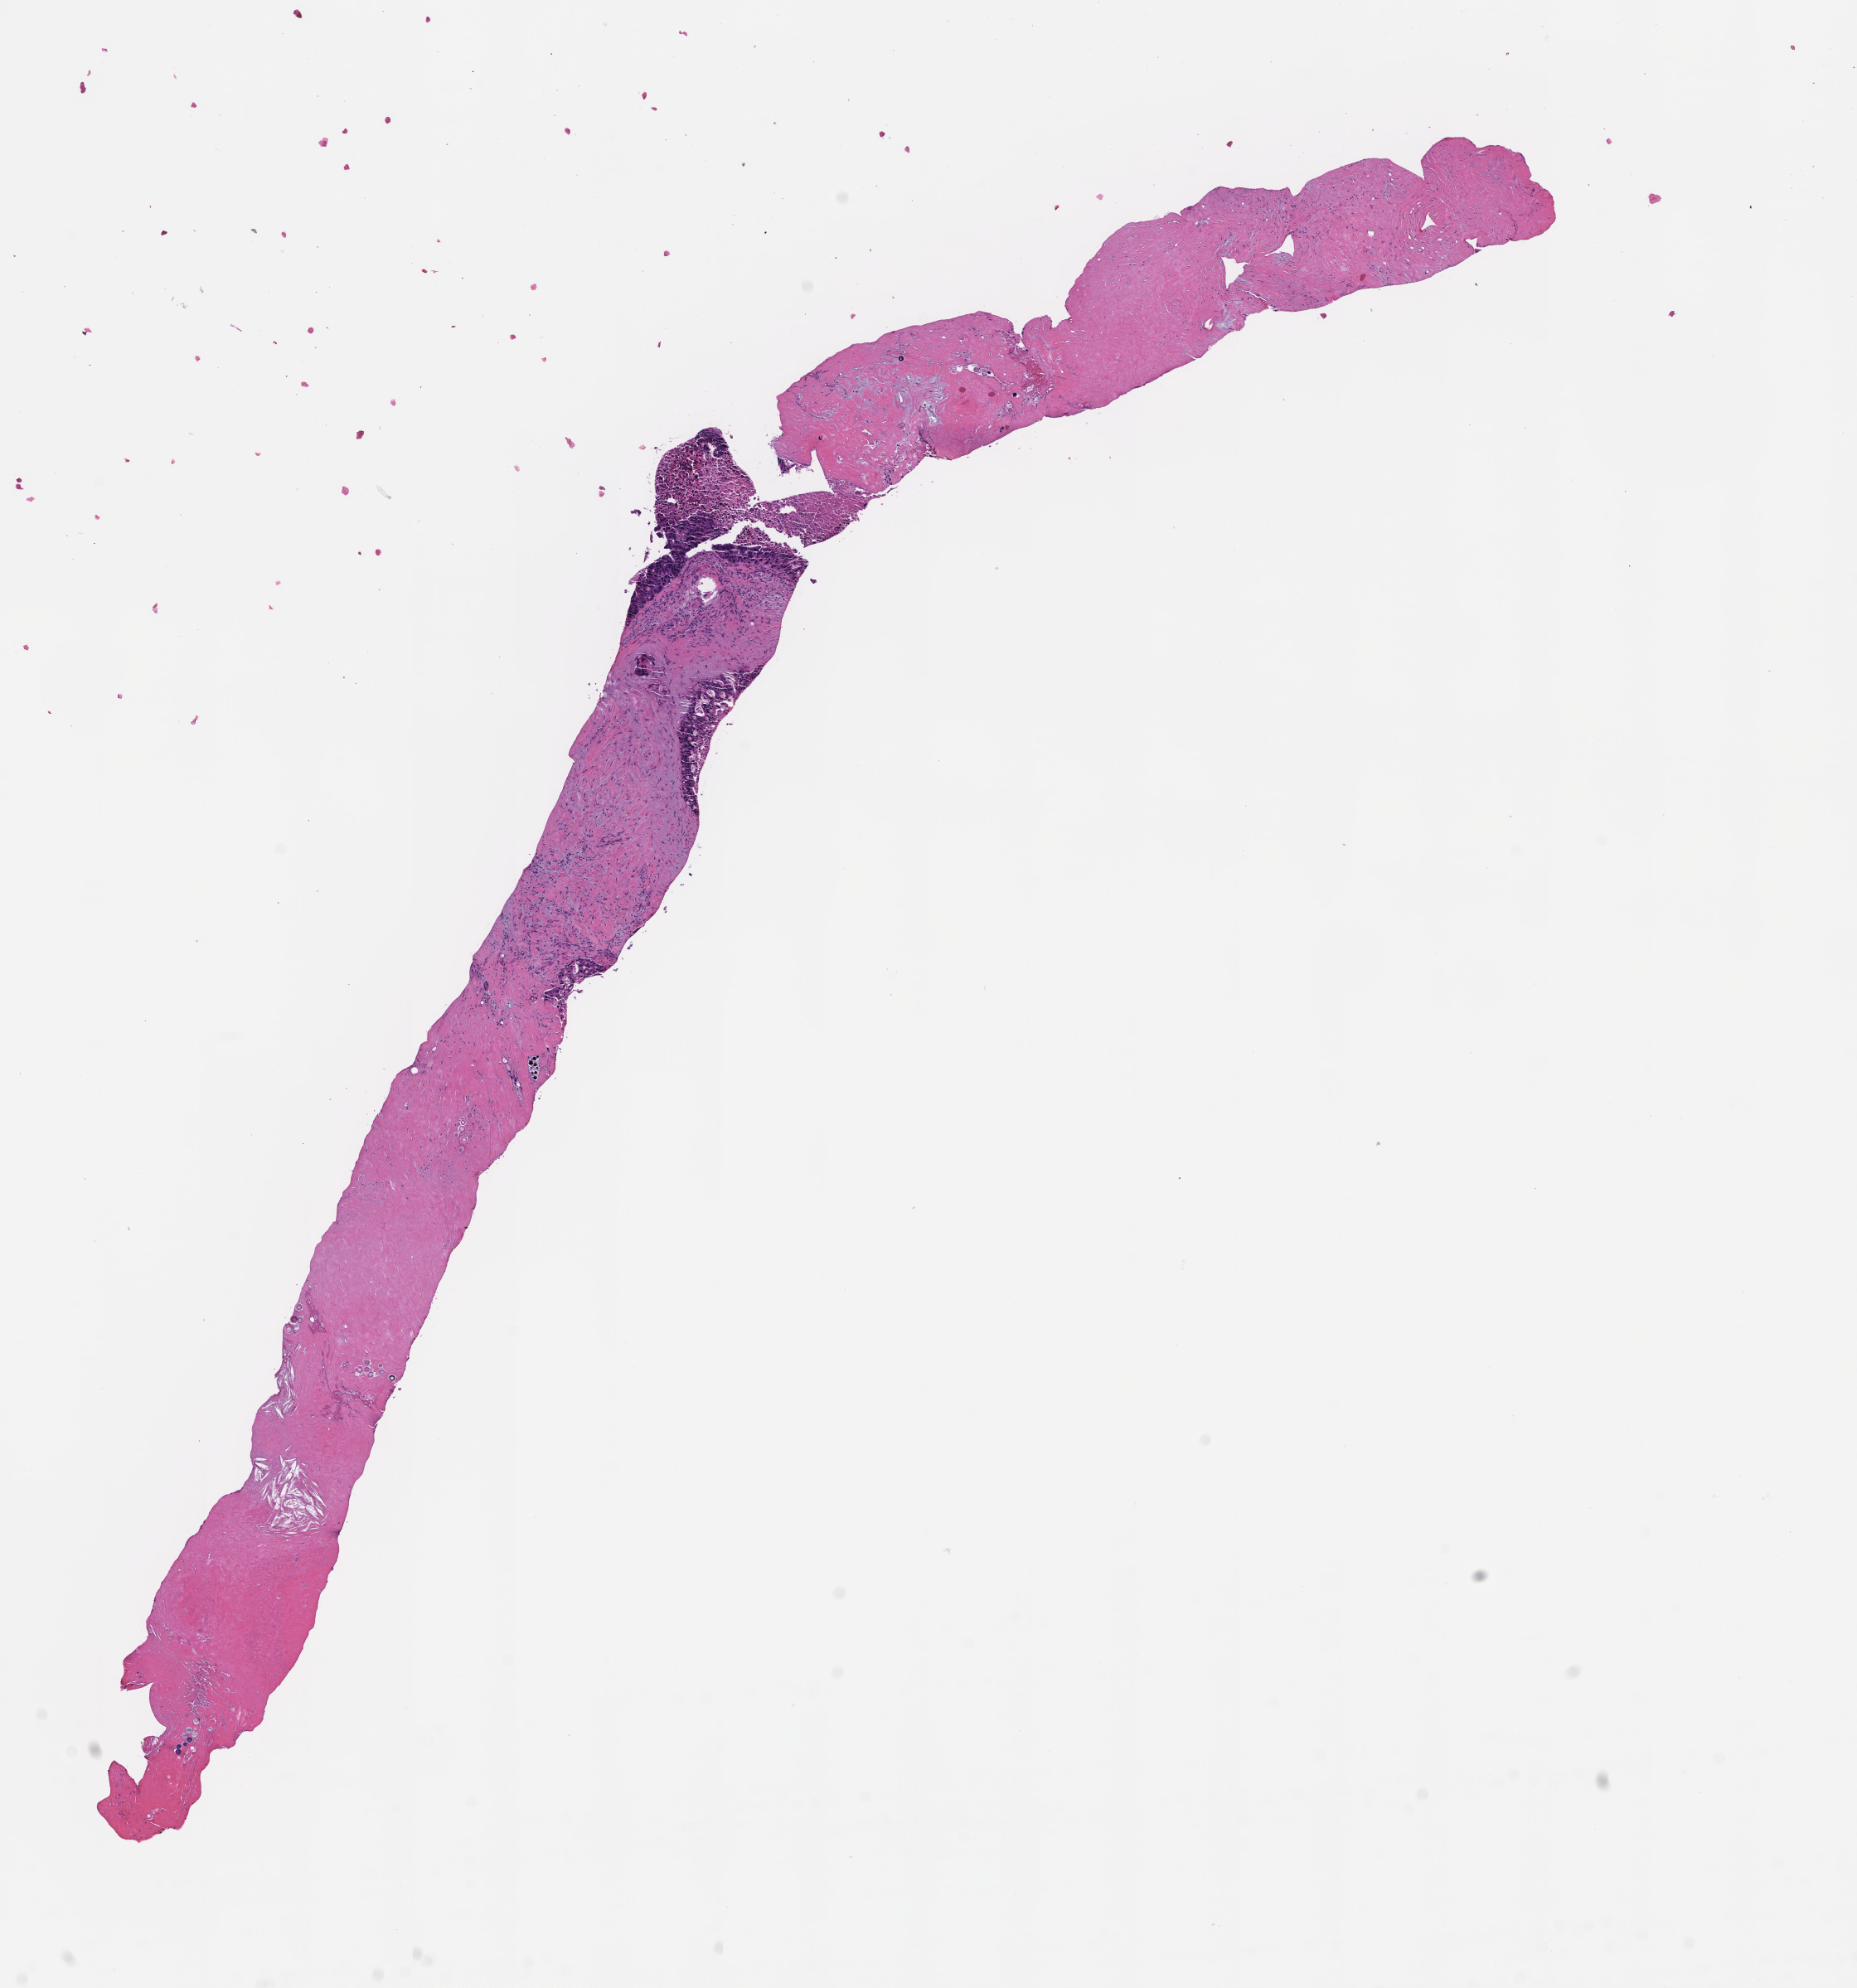
Haematoxylin and eosin whole-slide image, shown as a low-resolution overview of the whole scanned area (about 9.0 x 9.7 mm). Formalin-fixed, paraffin-embedded (FFPE) tissue. Specimen time point: collected at disease progression. Patient: male.
This section: metastatic tumor tissue. Primary diagnosis of the patient: Colorectal Carcinoma.